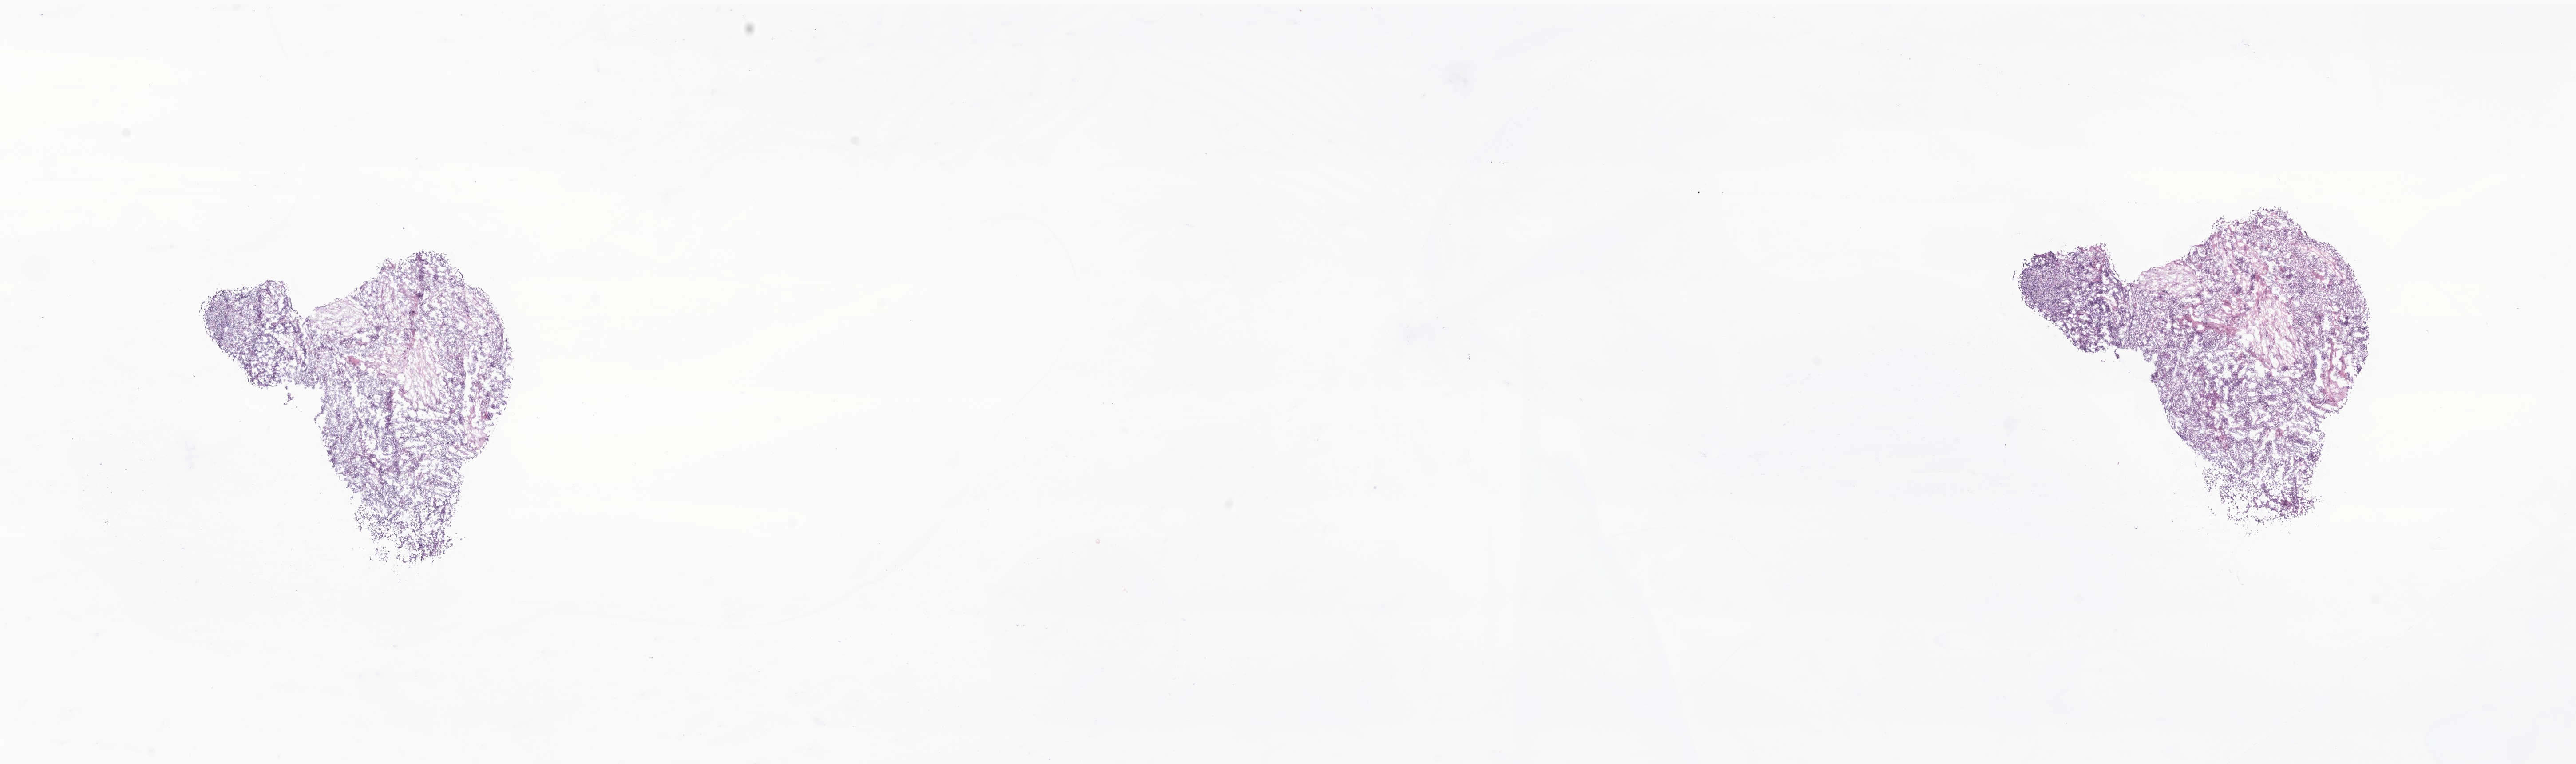
Whole-slide image, hematoxylin and eosin (H&E) stain of tumor tissue from the pelvis — low-resolution overview of the scanned area, about 24.5 x 7.3 mm. Frozen section (OCT-embedded). Patient: female, age 194 months (16 years 2 months).
- diagnosis: Sarcoma, NOS